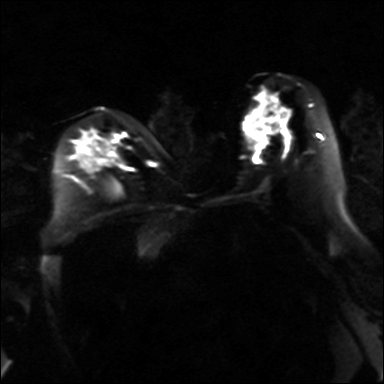
Breast MRI, one axial slice. Position 17 of 36 along the scan axis. Diffusion-weighted series; image 2 of 4 stored at this slice position (different b-values; order by instance number). 3 T. 384 × 384 image matrix, field of view 320 × 320 mm. Female patient.
Structures marked on this image (outlined manually by an expert reader):
- tumour on diffusion-weighted imaging: bounding box <255,107,275,130> (left, top, right, bottom; pixels)